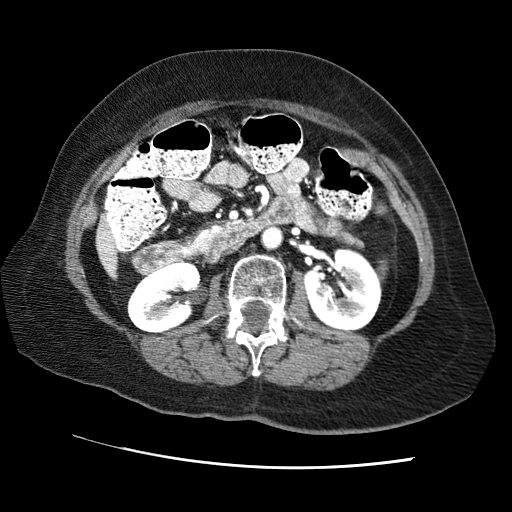
Contrast-enhanced abdominal CT (liver protocol), one axial slice; position 13 of 65 along the scan axis; reconstruction kernel STANDARD; 120 kVp; soft-tissue window (W 400 / L 40 HU); 2.5 mm slice thickness; 512 × 512 image matrix, field of view 340 × 340 mm. From the clinical record (not read from this slice): diagnosis: hepatocellular carcinoma (patient treated with transarterial chemoembolisation; whether this scan precedes or follows treatment is not stated here); TNM stage (as recorded): Stage-II; Child-Pugh class: A; tumour differentiation: no biopsy; tumour nodularity: multinodular.
Outlined on this slice (semi-automatic segmentation, software-assisted and operator-edited):
- liver parenchyma outside the tumour (the mass and vessels are separate outlines, so this box may not span the whole liver): bounding box <96,220,116,277> (left, top, right, bottom; pixels)
- liver vessels: <102,234,111,260>